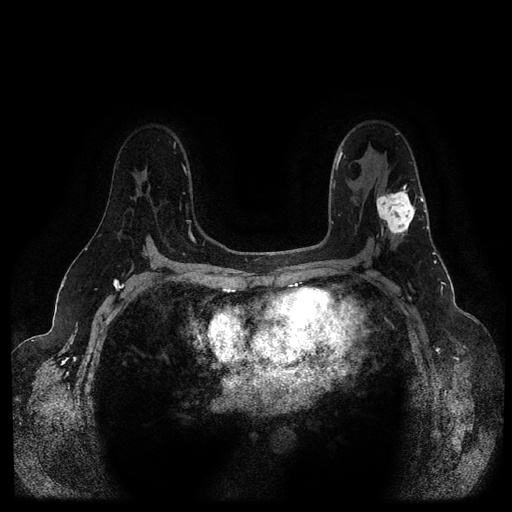
Breast MRI (dynamic contrast-enhanced, multi-phase), one axial slice; position 67 of 116 along the scan axis; dynamic contrast-enhanced series, time point 2 of 5 at this slice position (early post-contrast); 1.5 T; TE 2.6 ms, TR 5.3 ms; 2 mm slice thickness; 512 × 512 image matrix. Patient: female, 54 years.
Annotated regions visible in this slice (semi-automatic segmentation, software-assisted and operator-edited):
- breast lesion (labelled 'tumour' in the annotation; benign lesions carry a separate 'benign' label): box from (x=376, y=188) to (x=420, y=236) px